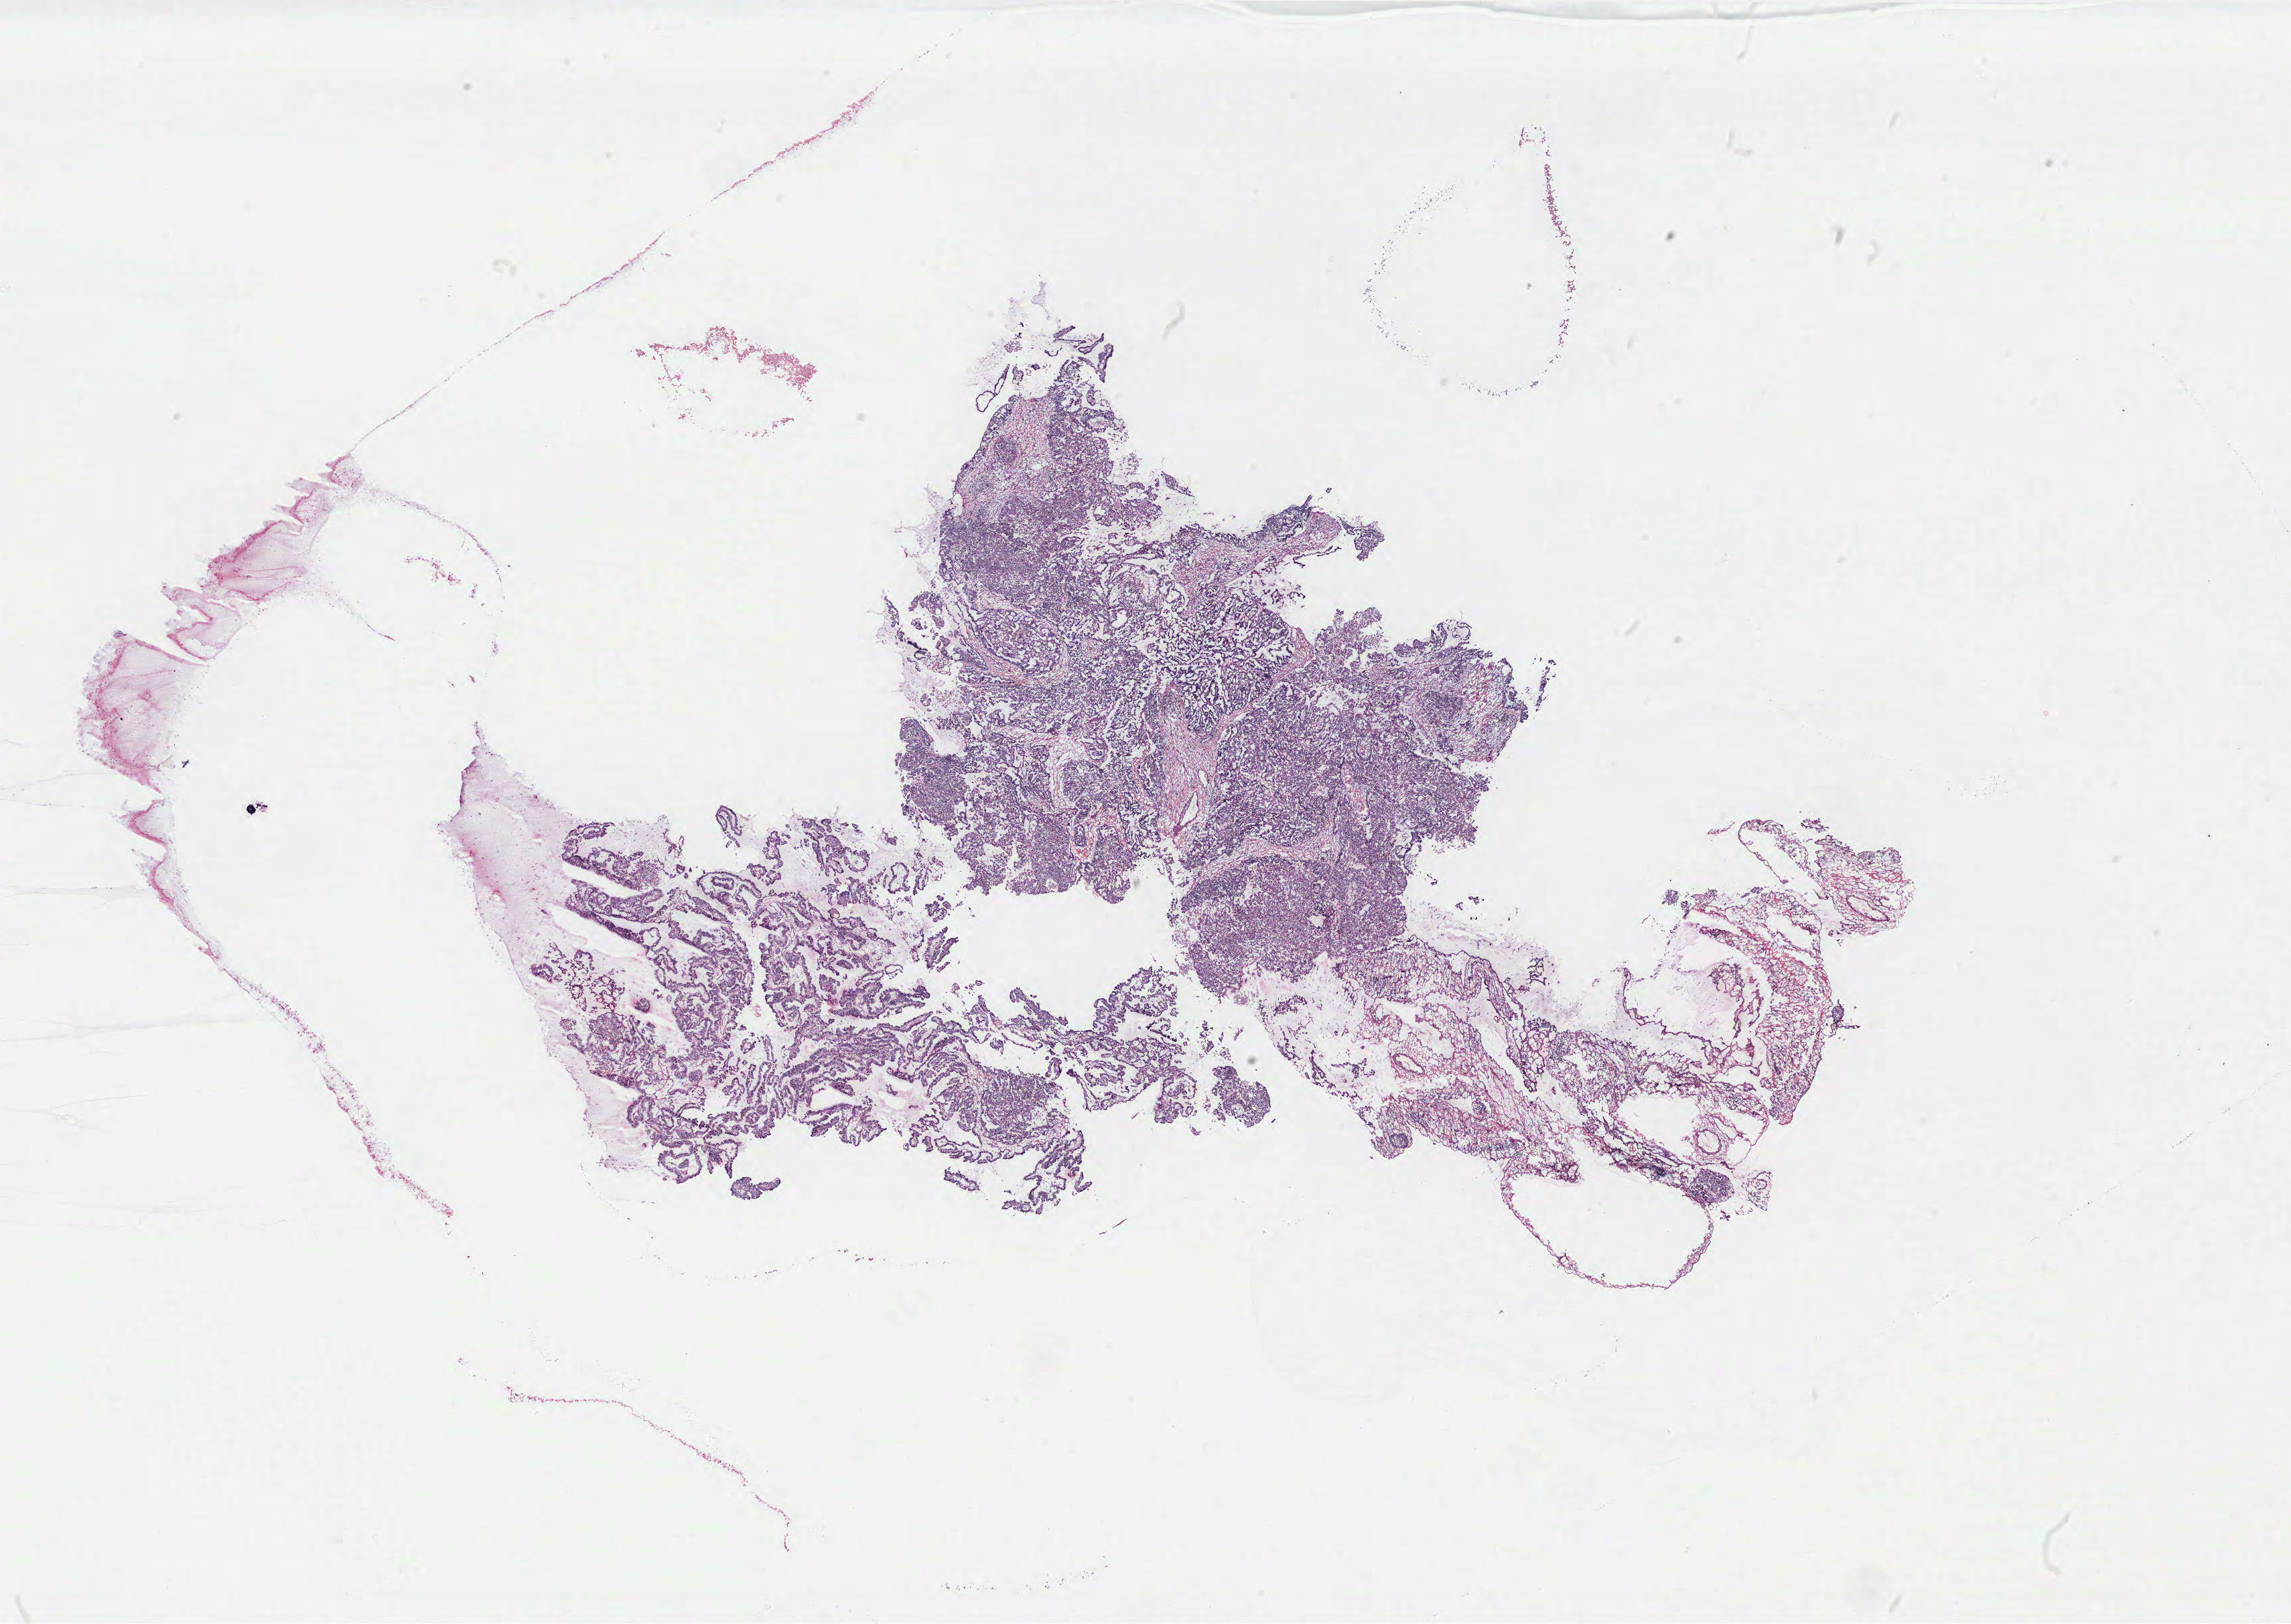
Whole-slide histology image, H&E-stained, a low-resolution overview of the entire scanned area, about 27.4 x 19.4 mm (acquisition: 40x scan), ovary, normal (non-tumour) tissue. 56-year-old female patient.
This section: normal (non-tumour) tissue from the same patient. Patient diagnosis: Serous adenocarcinoma, NOS.